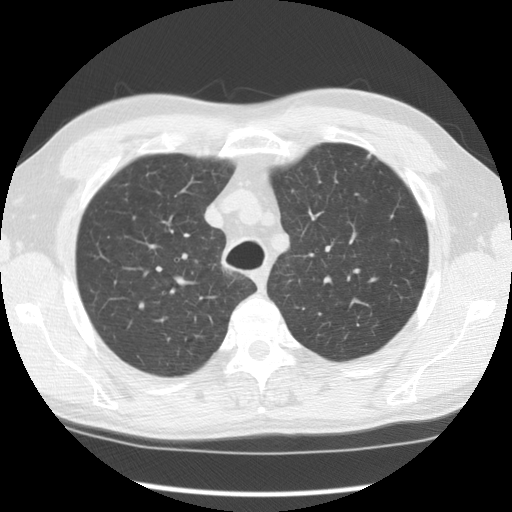
Axial slice from a low-dose chest CT screening exam. Baseline annual screen. Lung window (W 1500 / L -600 HU). 2.5 mm slice thickness. Slice 27 of 121 in the series. 512 × 512 image matrix. Male participant, aged 55 years at enrolment.
Lesion marked by an expert reader, bounding box [x1, y1, x2, y2] px = [347, 136, 386, 178]. Screening reader's record for this exam (one nodule recorded; not confirmed to be the boxed lesion): non-calcified nodule or mass ≥4 mm, left upper lobe, 5 × 5 mm, poorly defined margins, soft tissue attenuation. Official screen result: positive, change unspecified: nodule(s) >= 4 mm or enlarging nodule(s), mass(es), or other non-specific abnormalities suspicious for lung cancer. Lung cancer was diagnosed 159 days after this screen: adenocarcinoma, NOS, left upper lobe, moderately differentiated (G2), stage IA (AJCC 6th edition), 8 mm at pathology.